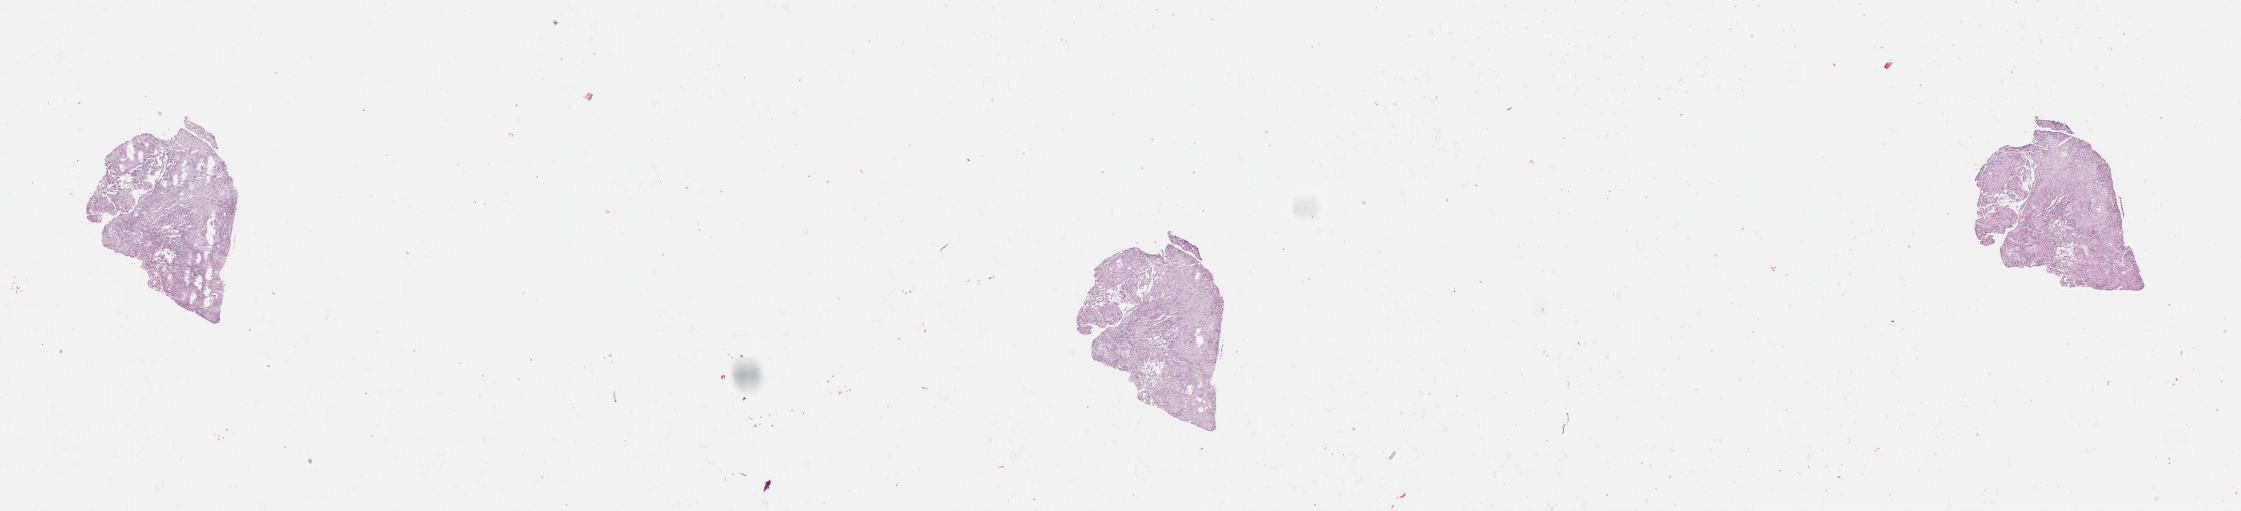
Digitized Hematoxylin and eosin (H&E) stained tissue section (whole slide) — shown as a low-resolution overview of the whole scanned area (about 36.1 x 8.2 mm), tumour tissue sample, sampled site: brain. 63-year-old female patient. Composition of this section per pathologist review: tumour nuclei 80%, necrosis 5%.
Diagnosis: Glioblastoma. Primary tumour site (as recorded): temporal lobe.